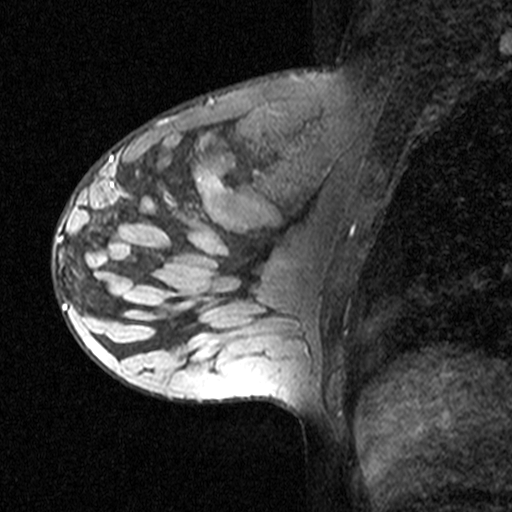
Breast MRI (dynamic contrast-enhanced), one sagittal slice; position 17 of 44 along the scan axis; dynamic contrast-enhanced study with each time point stored as its own series, time point 2 of 3 at this slice position (early post-contrast, ordered by acquisition time); 1.5 T; TE 4.5 ms, TR 11 ms; 3 mm slice thickness; 512 × 512 image matrix. Patient: female, 27 years. Case-level facts recorded for this patient, not image findings: setting: breast cancer imaged before/during neoadjuvant chemotherapy; receptor status: HR-positive, HER2-negative.
Outlined on this slice (semi-automatically segmented with operator editing):
- analysis volume of interest (the breast-tissue region the enhancement analysis was run in; not a lesion): box from (x=53, y=162) to (x=163, y=271) px
- tumour enhancement mask (voxels above the 90 % enhancement threshold inside the analysis volume of interest): (x=56, y=172)–(x=131, y=253)